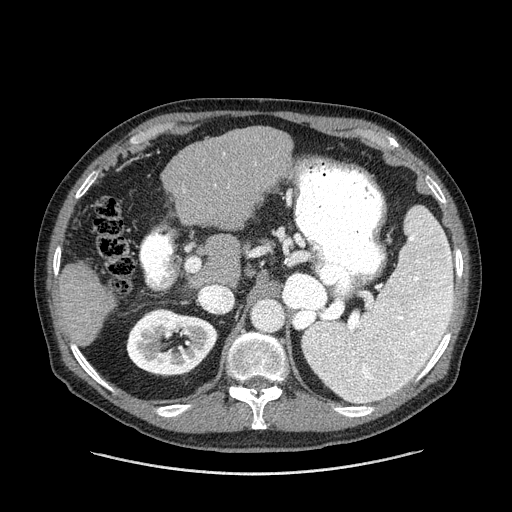
Contrast-enhanced abdominal CT (liver protocol), one axial slice. Reconstruction kernel STANDARD. 120 kVp. One of 2 acquisitions stored at this slice position. Soft-tissue window (W 400 / L 40 HU). 512 × 512 image matrix. From the clinical record (not read from this slice): diagnosis: hepatocellular carcinoma (patient treated with transarterial chemoembolisation; whether this scan precedes or follows treatment is not stated here); TNM stage (as recorded): Stage-II; Child-Pugh class: A; tumour differentiation: well differentiated; tumour nodularity: multinodular.
Annotated regions visible in this slice (semi-automatically segmented with operator editing):
- liver parenchyma outside the tumour (the mass and vessels are separate outlines, so this box may not span the whole liver): box from (x=56, y=126) to (x=292, y=346) px
- liver vessels: (x=183, y=153)–(x=225, y=191)